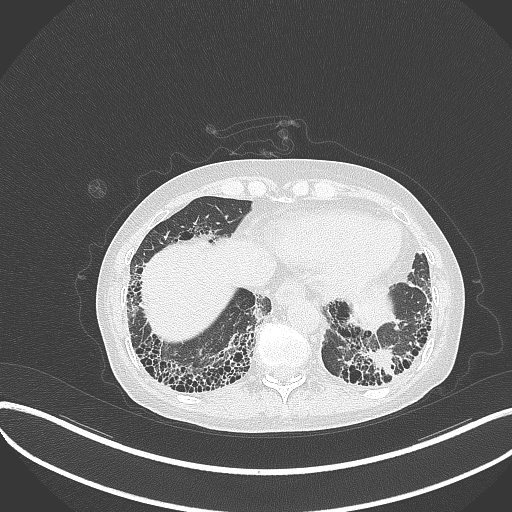
Chest CT, one axial slice; position 65 of 373 along the scan axis; 120 kVp; lung window (W 1500 / L -600 HU); 512 × 512 image matrix, field of view 400 × 400 mm. Patient: female, 56 years. From the clinical record (not read from this slice): clinical TNM (as recorded): T1 N0 M0.
Outlined on this slice (rectangle marked by the reading radiologist):
- lung tumour (recorded histology: adenocarcinoma): bounding box <361,348,399,386> (left, top, right, bottom; pixels)